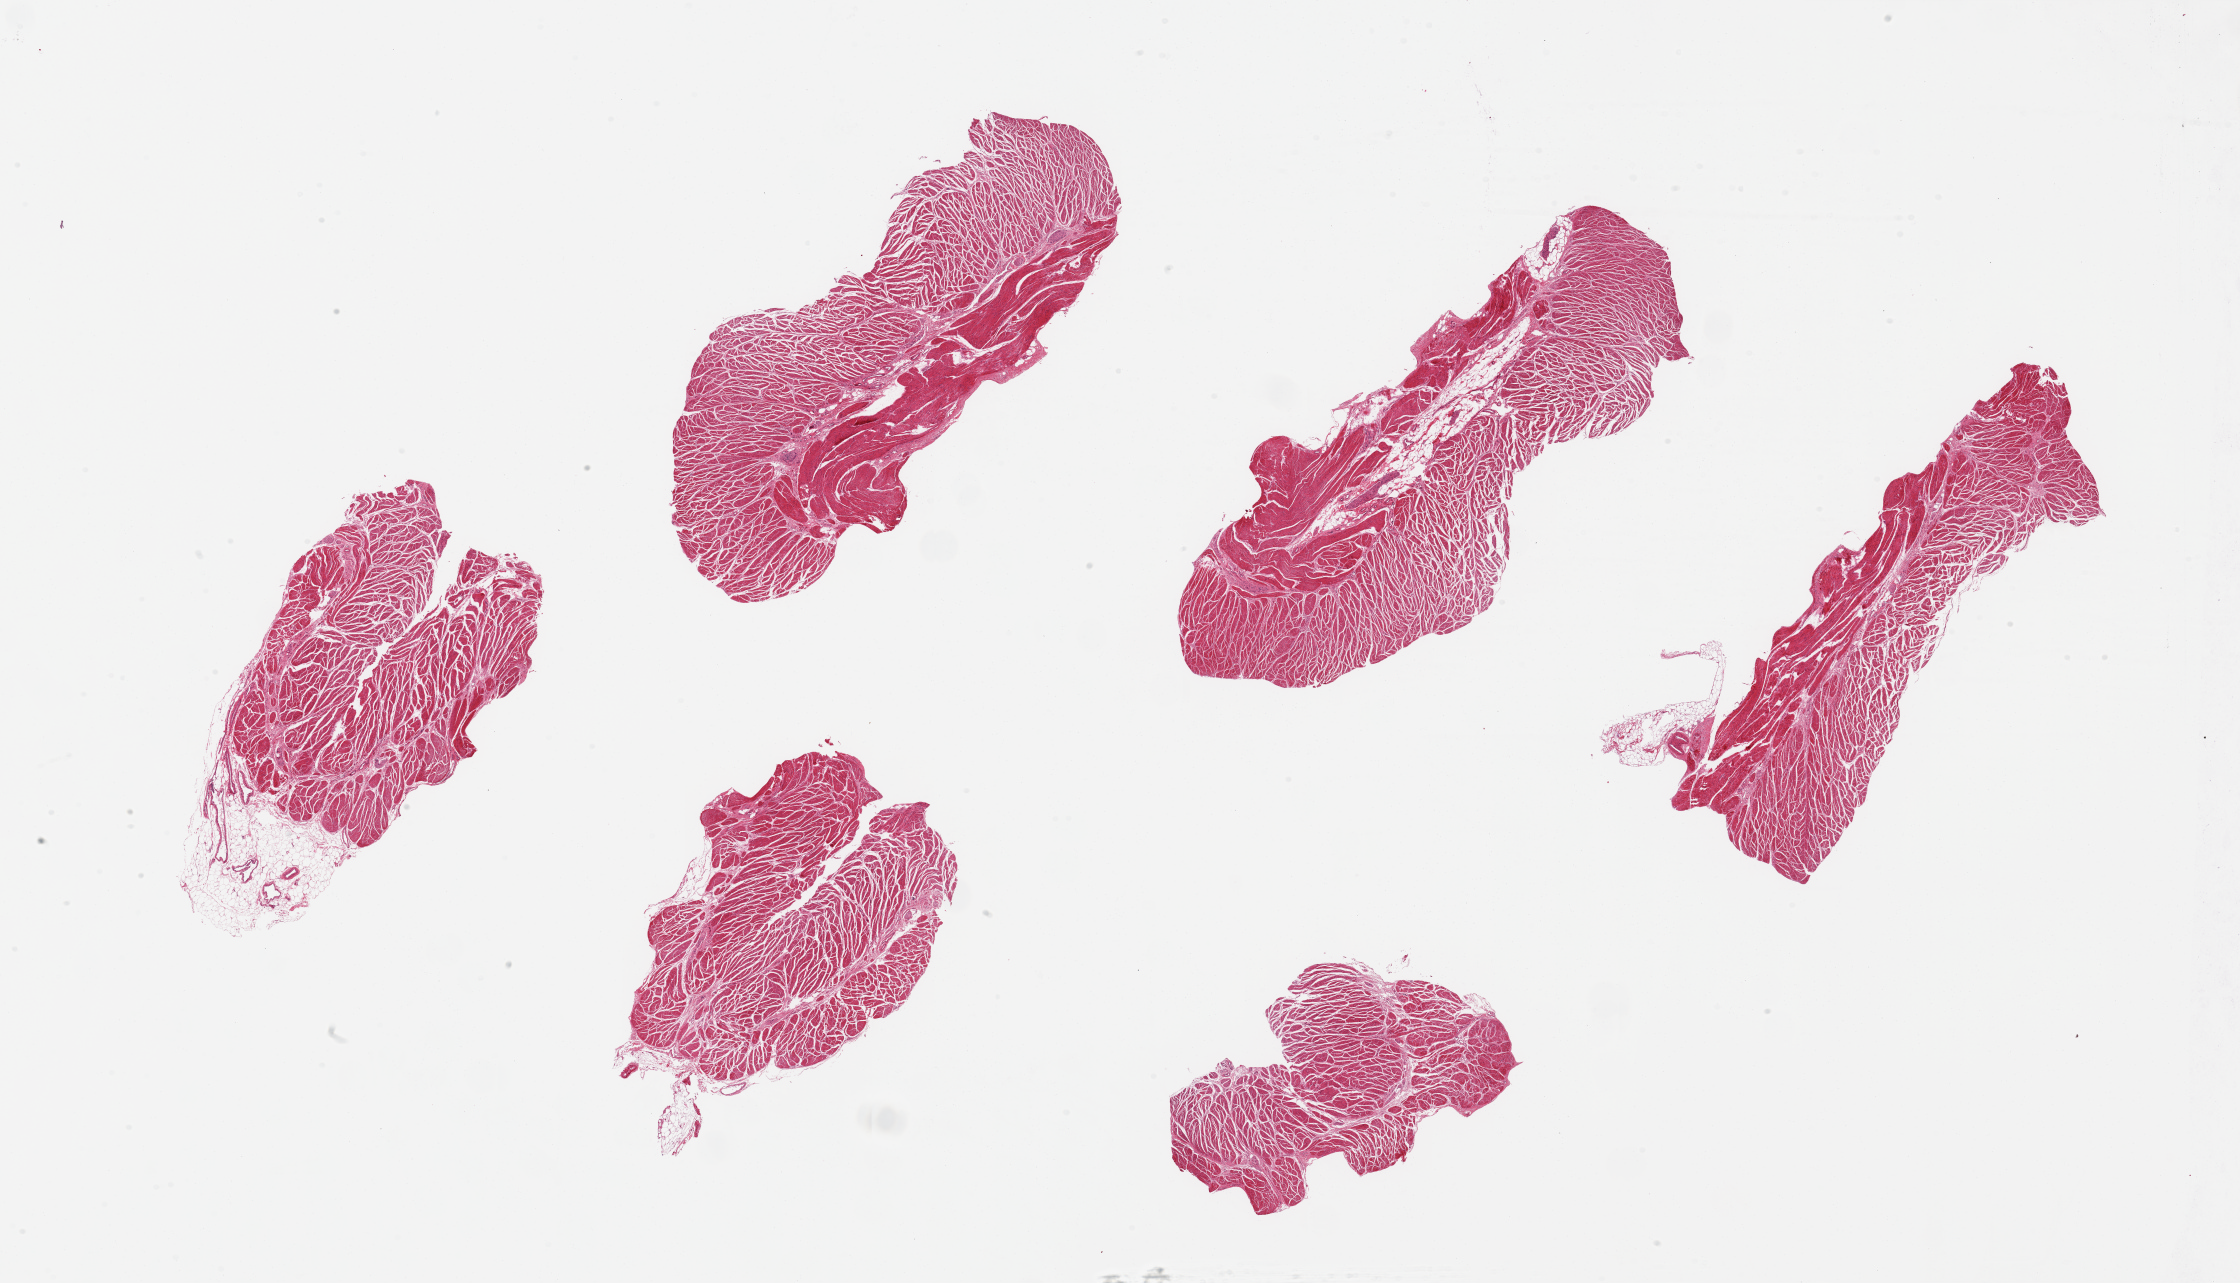
Haematoxylin and eosin whole-slide image — a low-resolution overview of the entire scanned area, about 35.4 x 20.3 mm (from a 20x scan), PAXgene-fixed paraffin-embedded (PFPE) section, section of esophageal muscle (target tissue), tissue donor sample. Donor sex: male.
Review note (as recorded): 6 pieces ~10x4mm.